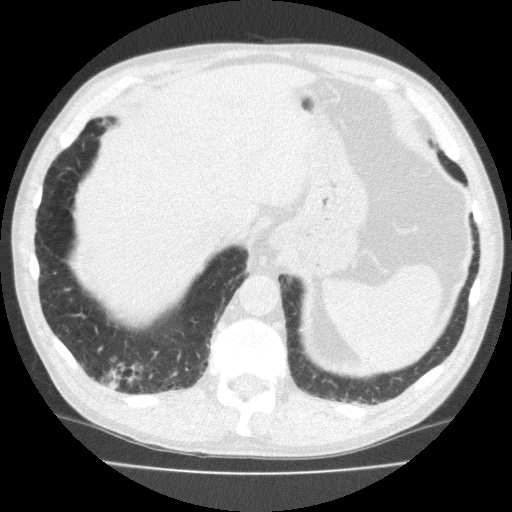
Low-dose screening chest CT, one axial slice; position 46 of 195 along the scan axis; lung window (W 1500 / L -600 HU); 2 mm slice thickness; 512 × 512 image matrix, field of view 350 × 350 mm.
Structures marked on this image (manually delineated by an expert):
- lesion 1 (tumor, lower lobe of right lung): bounding box (x1, y1, x2, y2) in pixels: (106, 363, 142, 393)